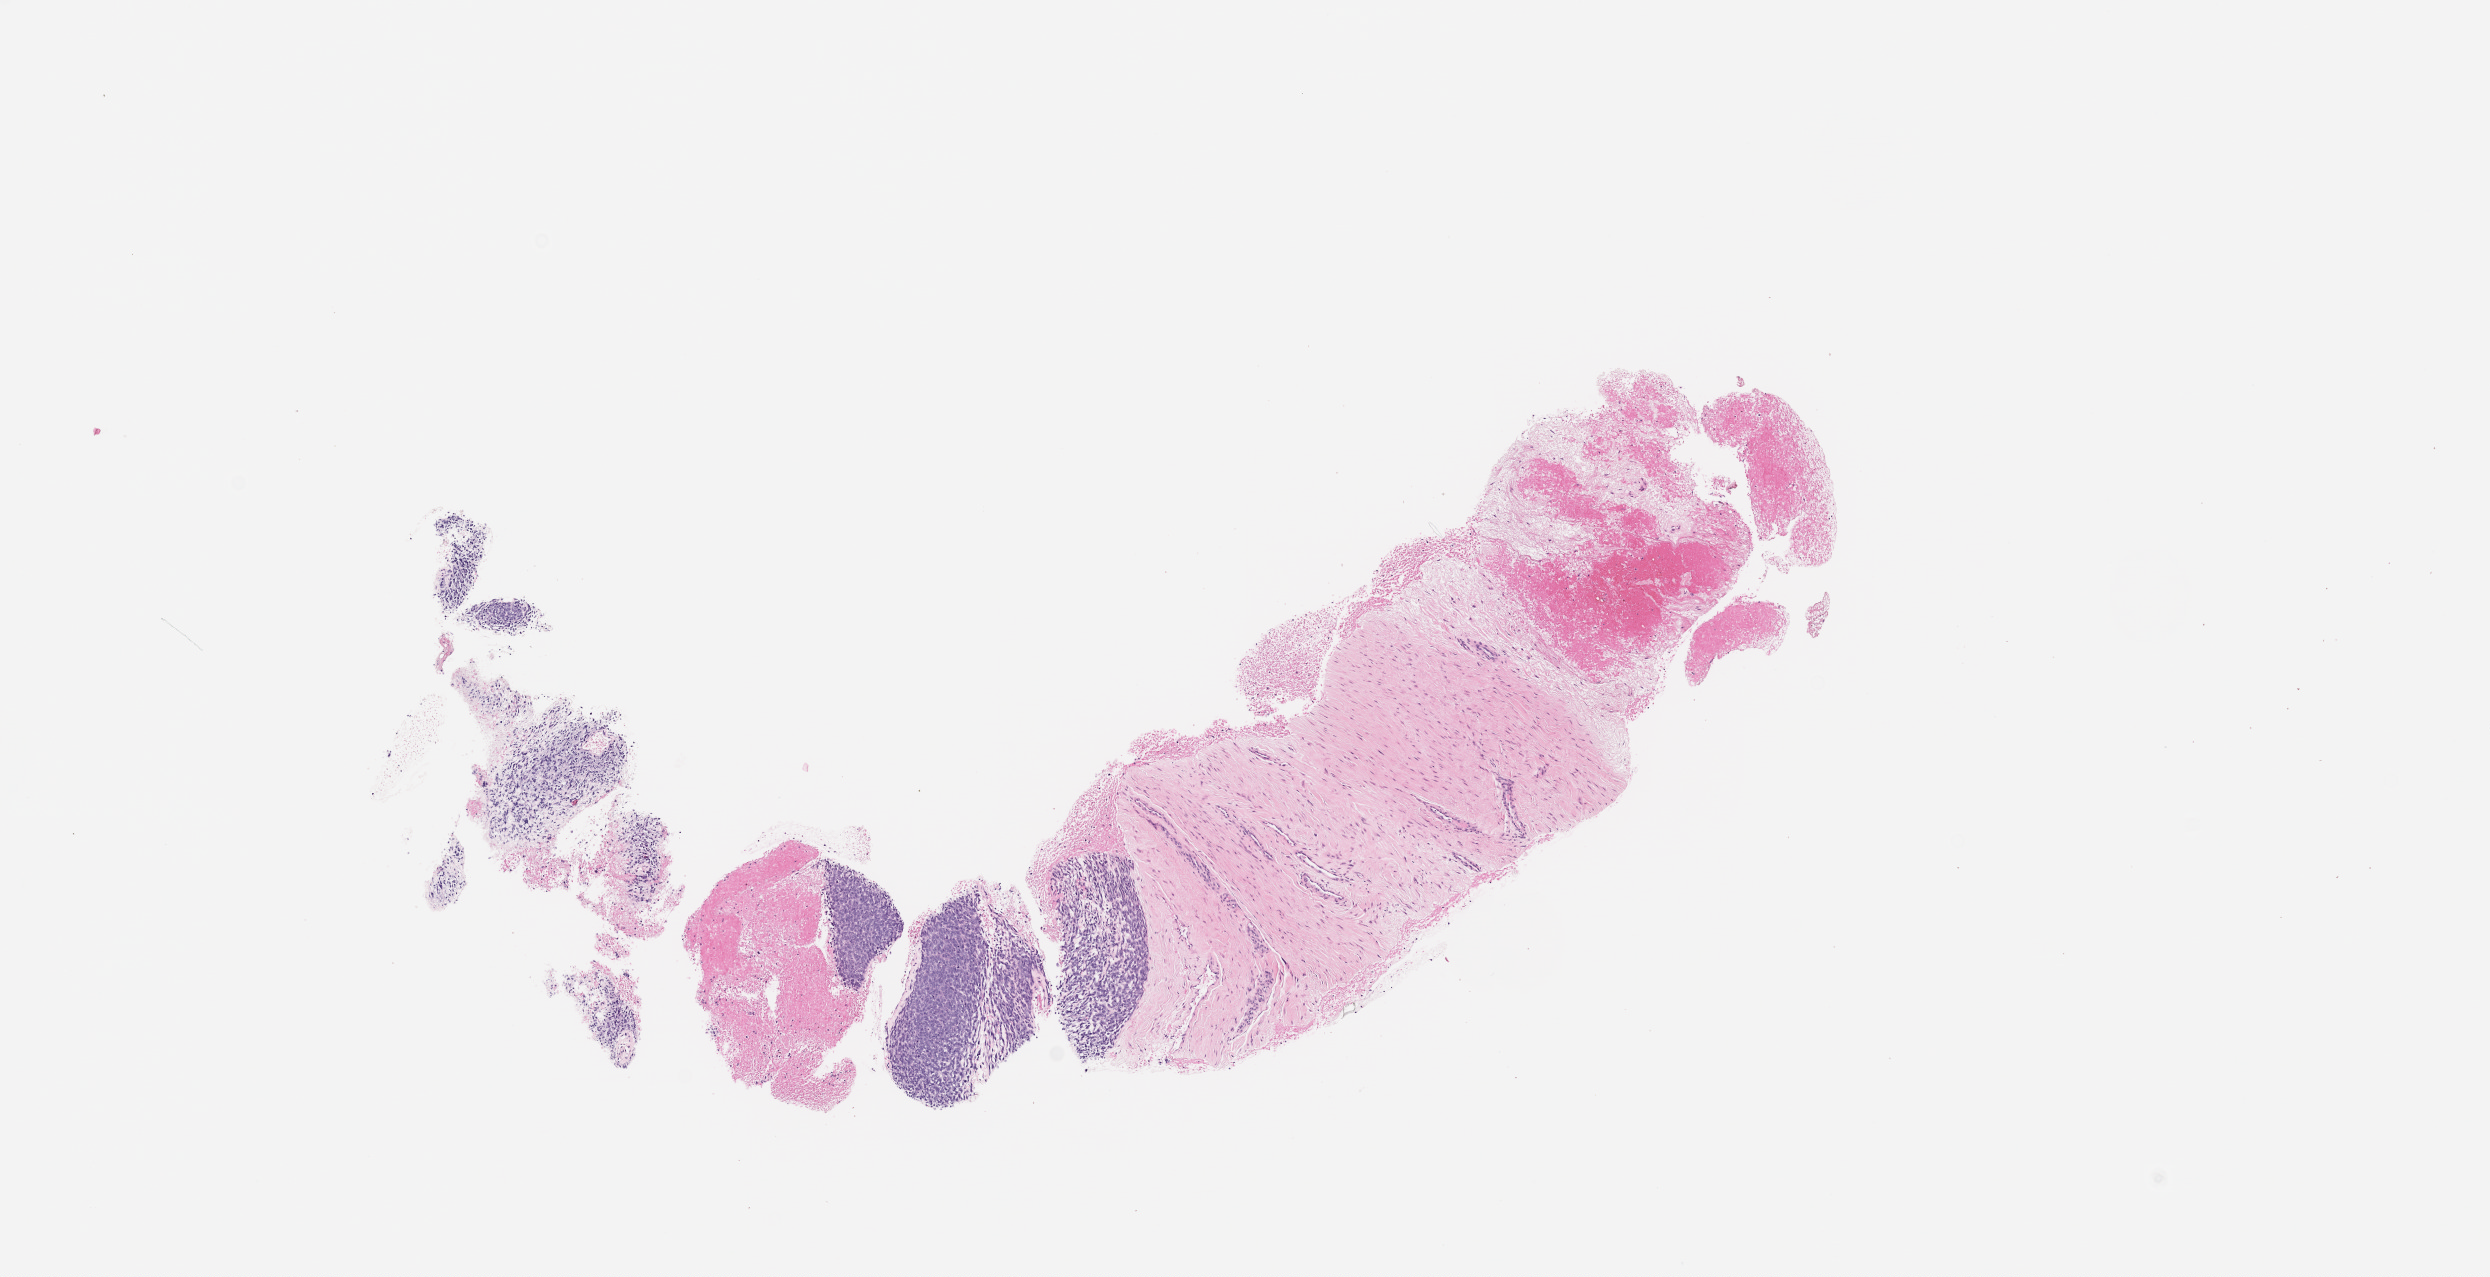
H&E whole-slide image of the patient's (originator) tumor tissue, shown as a low-resolution overview of the whole scanned area (about 10.0 x 5.1 mm), FFPE section, originating tumor site category: musculoskeletal. Male patient, aged 39.
- diagnosis: Synovial Sarcoma